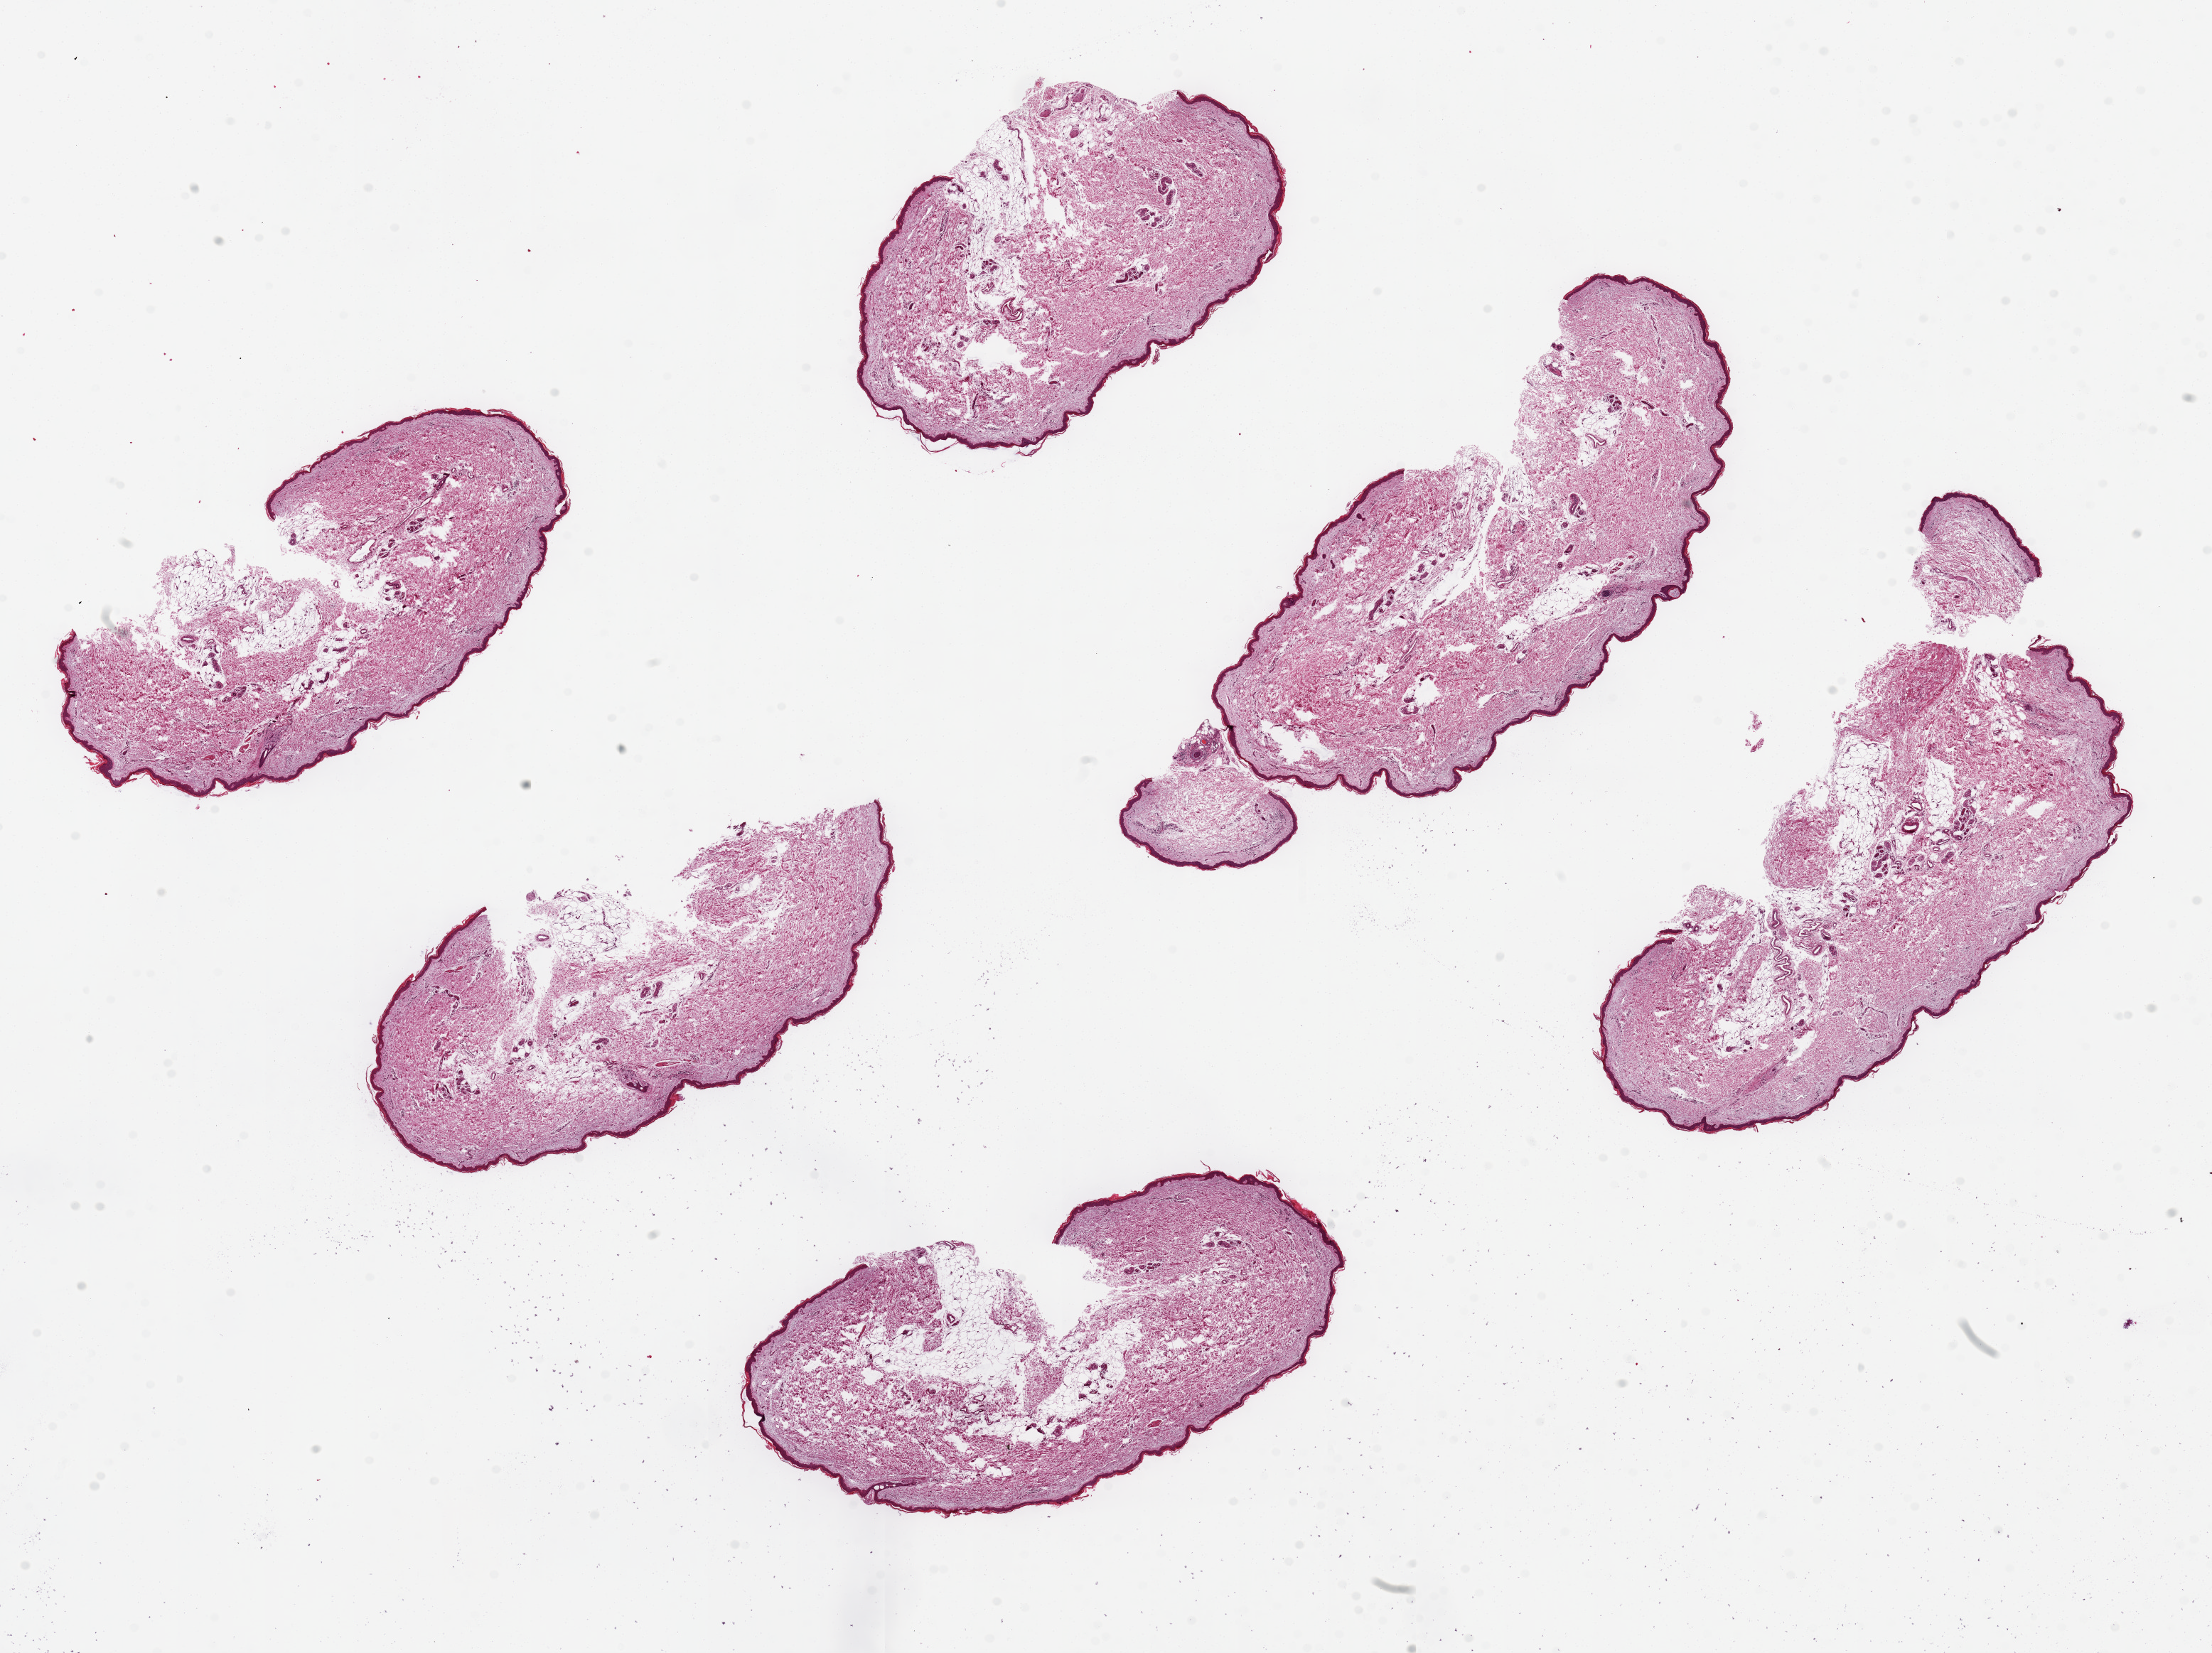
Whole-slide image, haematoxylin and eosin stain, shown as a low-resolution overview of the whole scanned area (about 24.6 x 18.4 mm, acquisition: 20x scan), PAXgene-fixed, paraffin-embedded tissue, sampled site (target tissue): skin of lower leg, tissue donor sample. Male donor.
Pathologist's review note for this sample: 6 ~6.5x2.5mm pieces; squamous epithelium is ~1--2% of thickness.